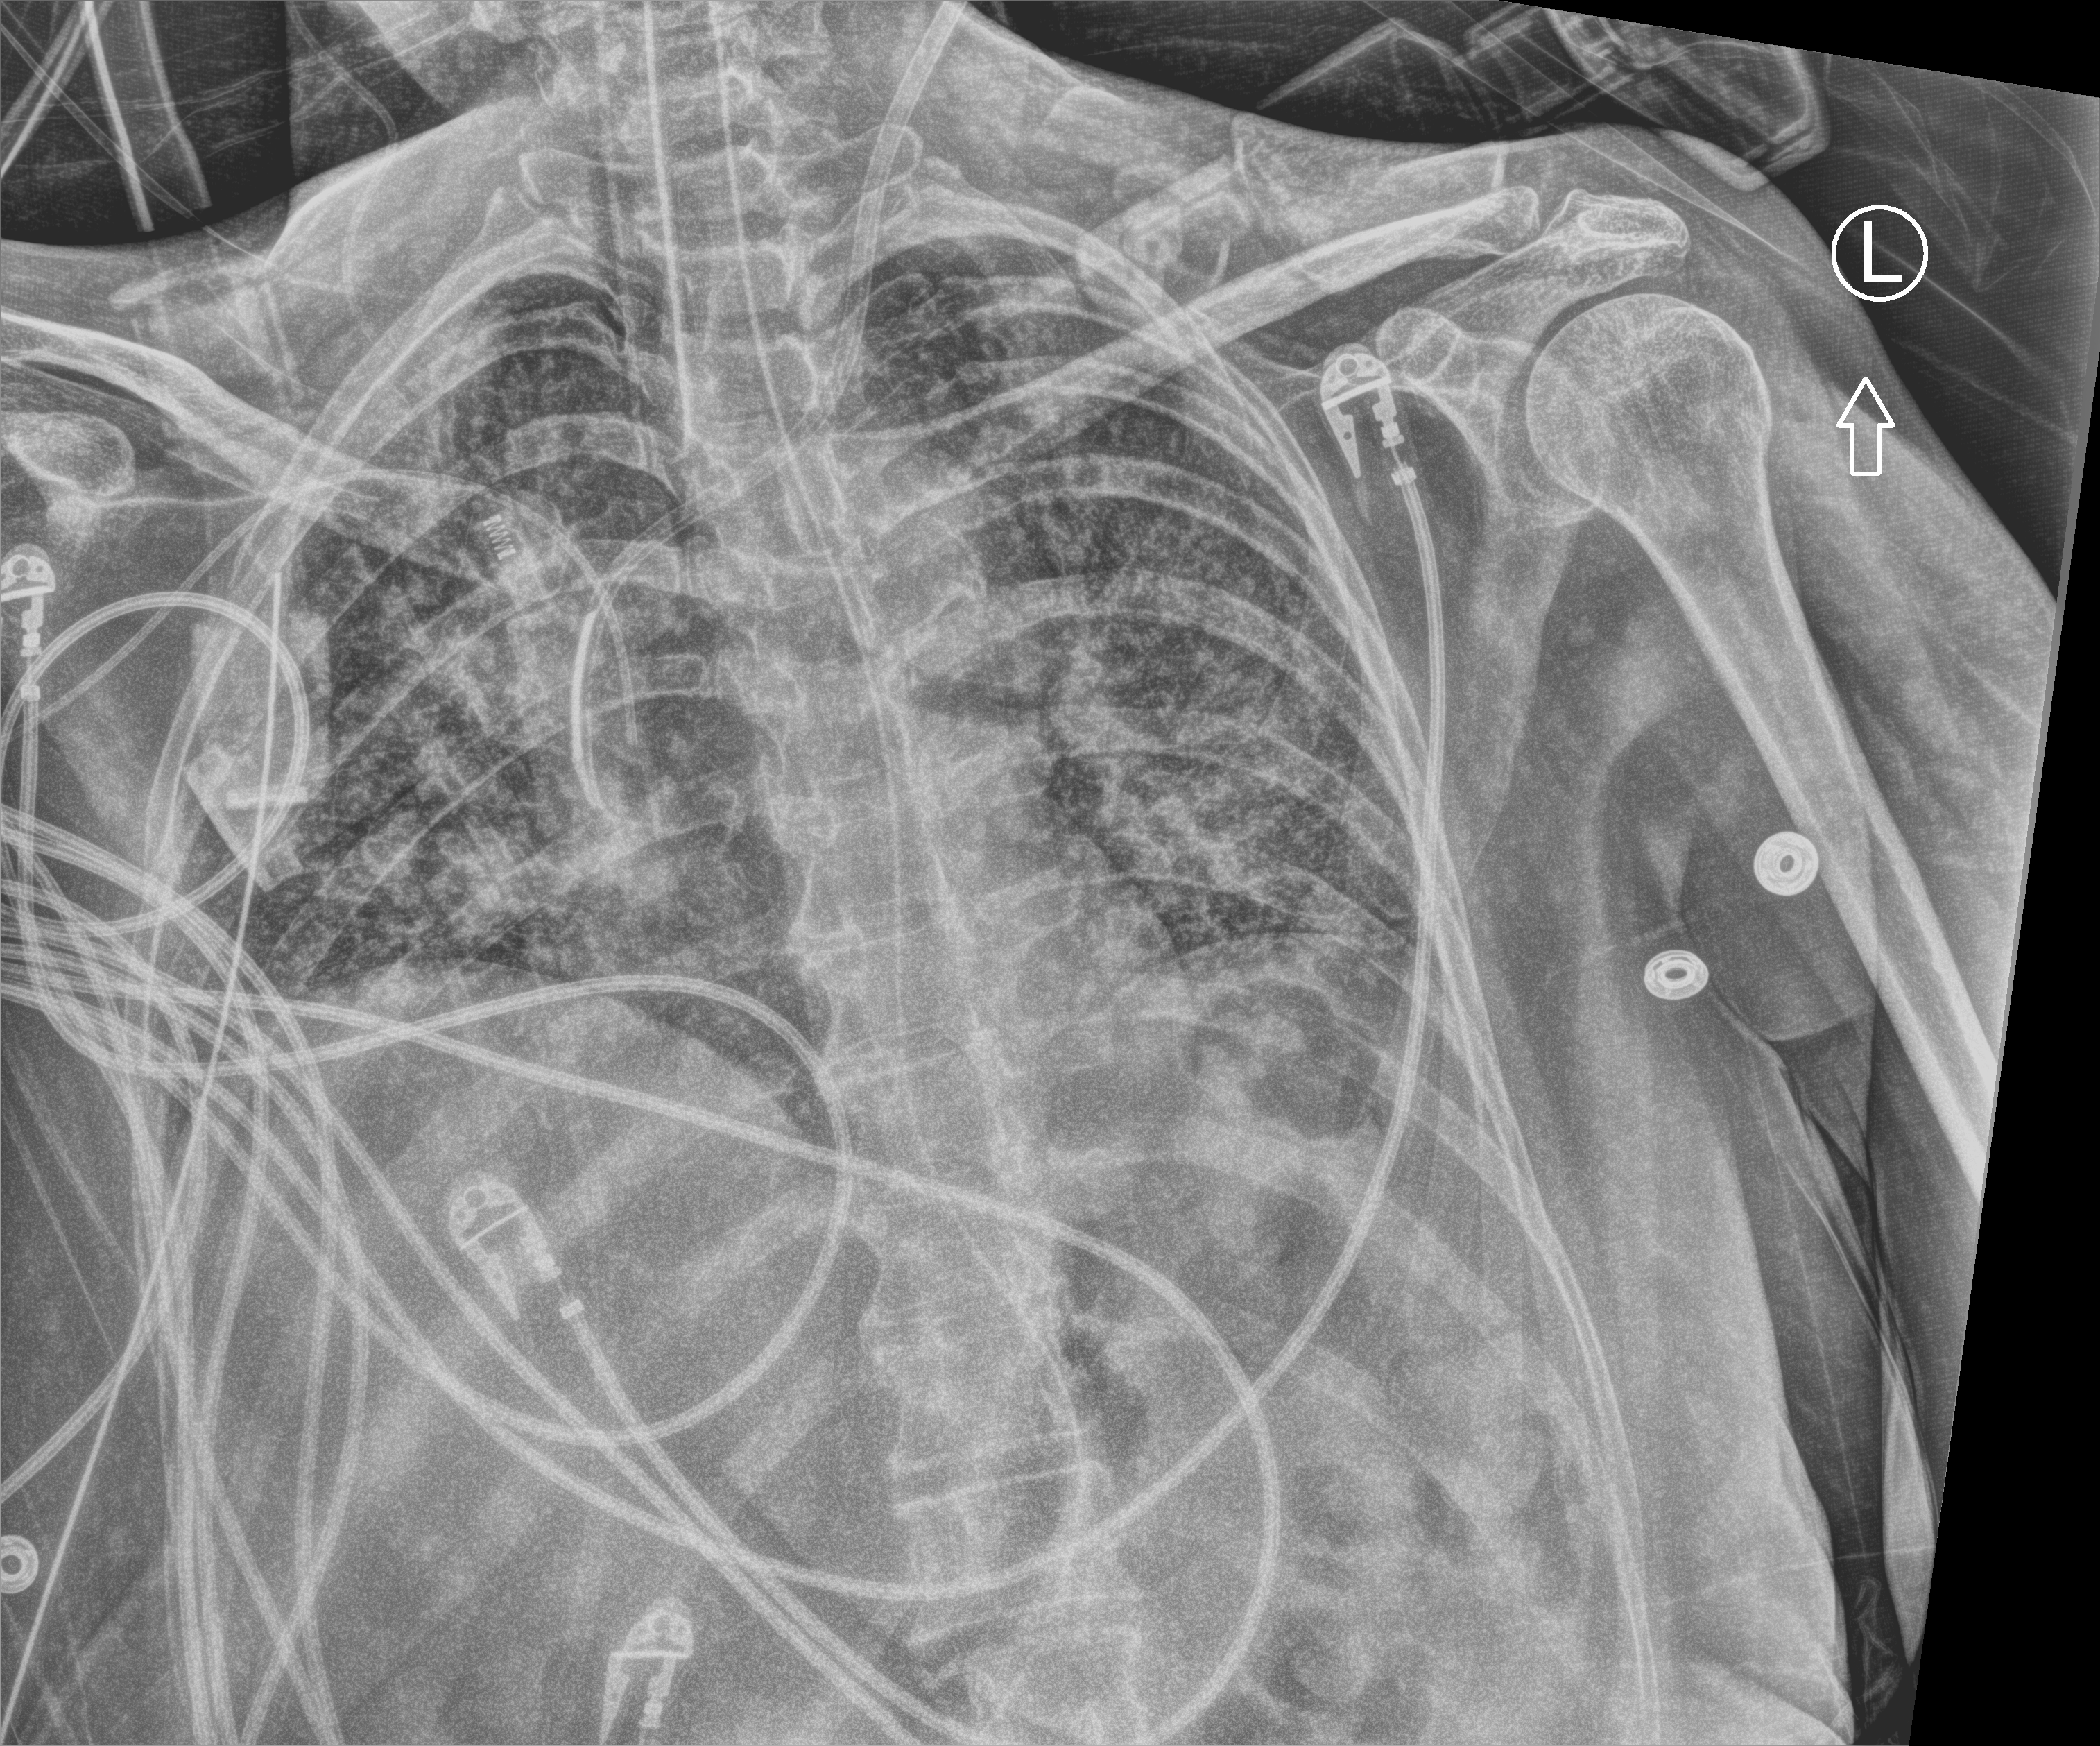
Portable chest radiograph, anteroposterior (AP) projection. Female patient hospitalised with COVID-19, age 60–74 years.
From the hospital-stay record, not from the radiograph (when in the stay this image was taken is not recorded): mechanically ventilated during this hospital stay: yes.